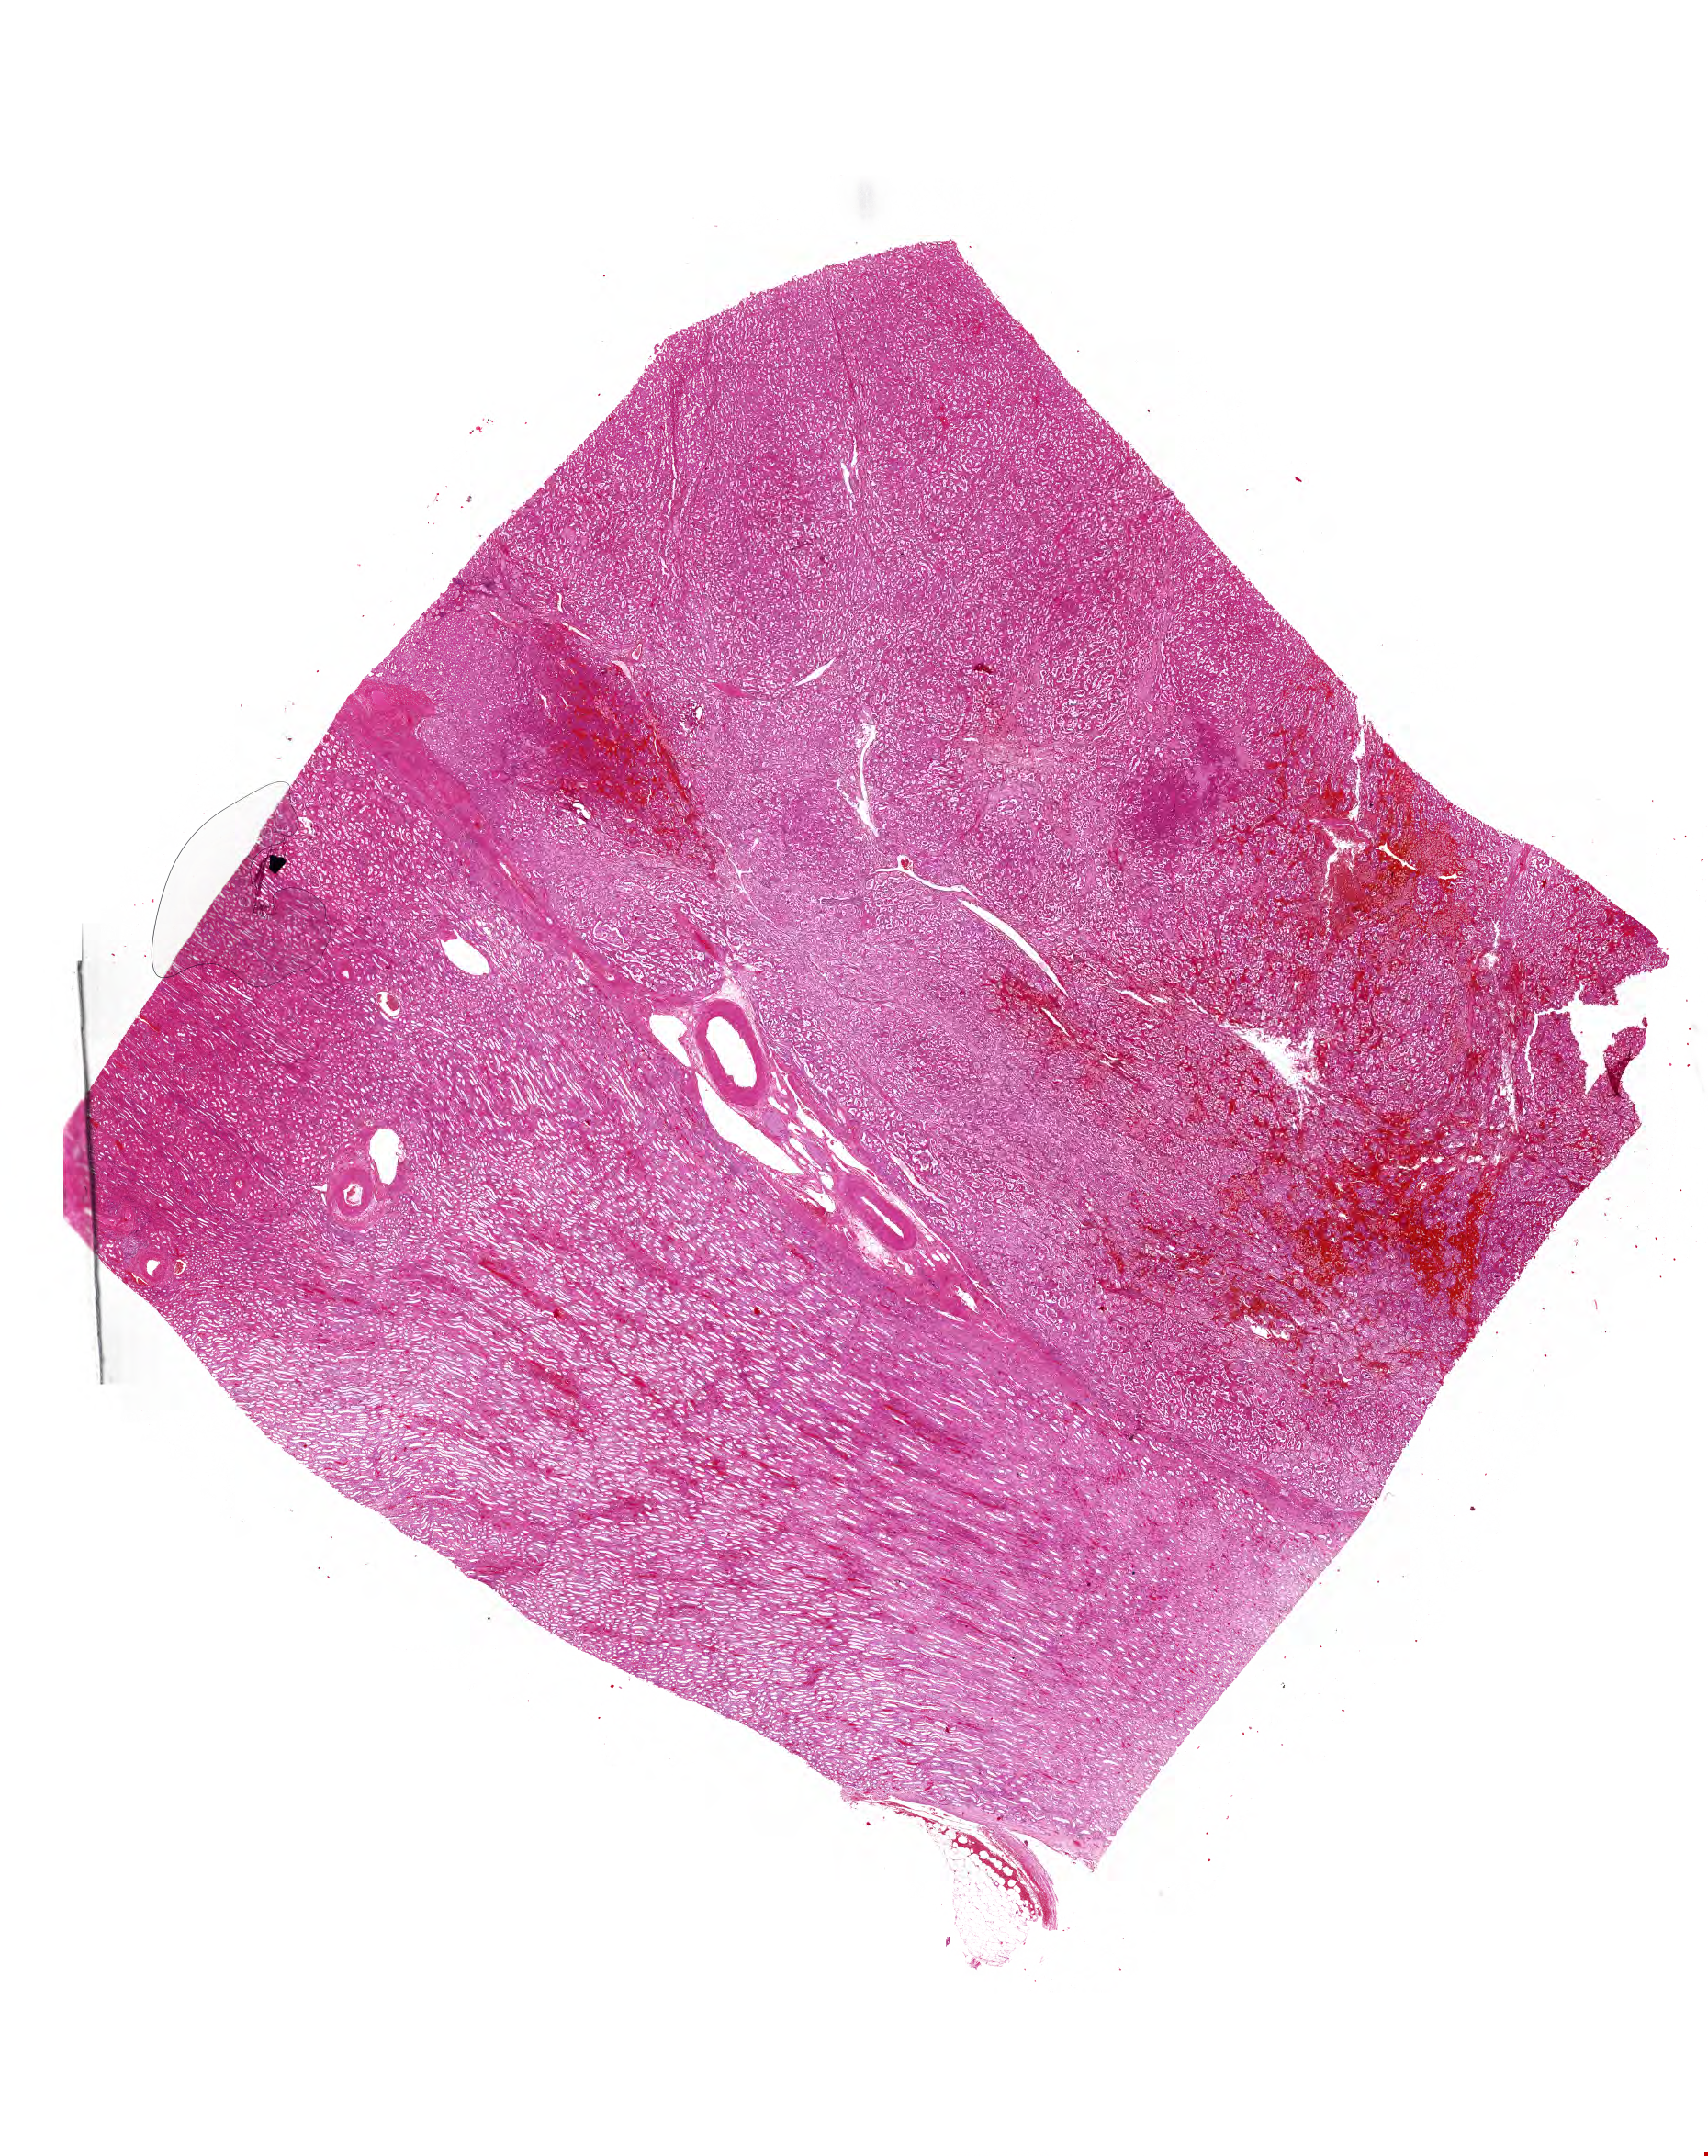
H&E whole-slide image, low-resolution overview of the scanned area, about 23.2 x 29.2 mm (acquisition: 40x scan); formalin-fixed paraffin-embedded (FFPE) diagnostic section; primary tumour sample from the kidney. Female patient; age at initial diagnosis 51 years.
Laterality: right. Diagnosis: Papillary adenocarcinoma, NOS.